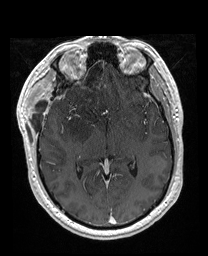
Brain MRI from a brain-tumour surgery series, one axial slice; slice 102 of 176 in the series (ordered by position); T1-weighted post-contrast; 1 mm slice thickness; 208 × 256 image matrix, field of view 208 × 256 mm. Case-level facts recorded for this patient, not image findings: histopathology: Astrocytoma; WHO grade: 4; IDH mutation: yes.
Annotated regions visible in this slice (expert manual segmentation):
- previous resection cavity: box from (x=72, y=55) to (x=91, y=83) px